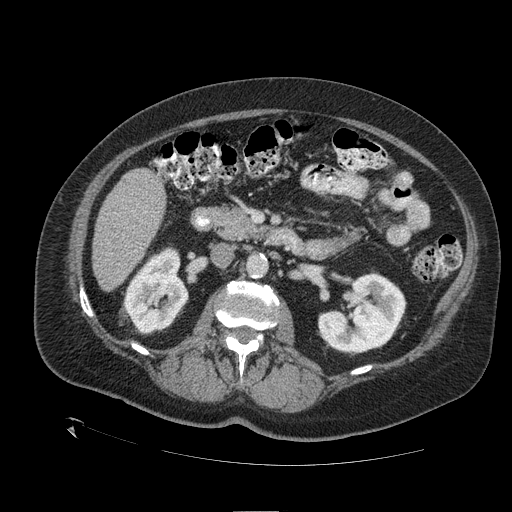
Contrast-enhanced abdominal CT (liver protocol), one axial slice. Position 46 of 109 along the scan axis. 120 kVp. One of 2 acquisitions stored at this slice position. Soft-tissue window (W 400 / L 40 HU). 2.5 mm slice thickness. 512 × 512 image matrix, field of view 460 × 460 mm. Case-level facts recorded for this patient, not image findings: diagnosis: hepatocellular carcinoma (patient treated with transarterial chemoembolisation; whether this scan precedes or follows treatment is not stated here); TNM stage (as recorded): Stage-I; Child-Pugh class: A; tumour differentiation: no biopsy; tumour nodularity: uninodular.
Outlined on this slice (semi-automatic segmentation, software-assisted and operator-edited):
- liver parenchyma outside the tumour (the mass and vessels are separate outlines, so this box may not span the whole liver): bounding box <92,168,166,290> (left, top, right, bottom; pixels)